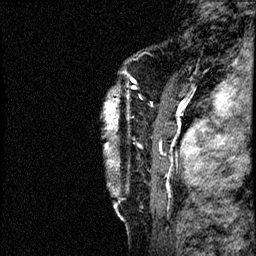
Breast MRI (dynamic contrast-enhanced), one sagittal slice. Dynamic contrast-enhanced study with each time point stored as its own series, time point 2 of 4 at this slice position (early post-contrast, ordered by acquisition time). 1.5 T. TE 4.2 ms, TR 17.6 ms. 2 mm slice thickness. 256 × 256 image matrix. Female patient, age 40 years. Case-level facts recorded for this patient, not image findings: setting: breast cancer imaged before/during neoadjuvant chemotherapy; receptor status: HER2-positive.
Structures marked on this image (semi-automatically segmented with operator editing):
- analysis volume of interest (the breast-tissue region the enhancement analysis was run in; not a lesion): bounding box <103,56,197,205> (left, top, right, bottom; pixels)
- tumour enhancement mask (voxels above the 100 % enhancement threshold inside the analysis volume of interest): <104,74,197,168>